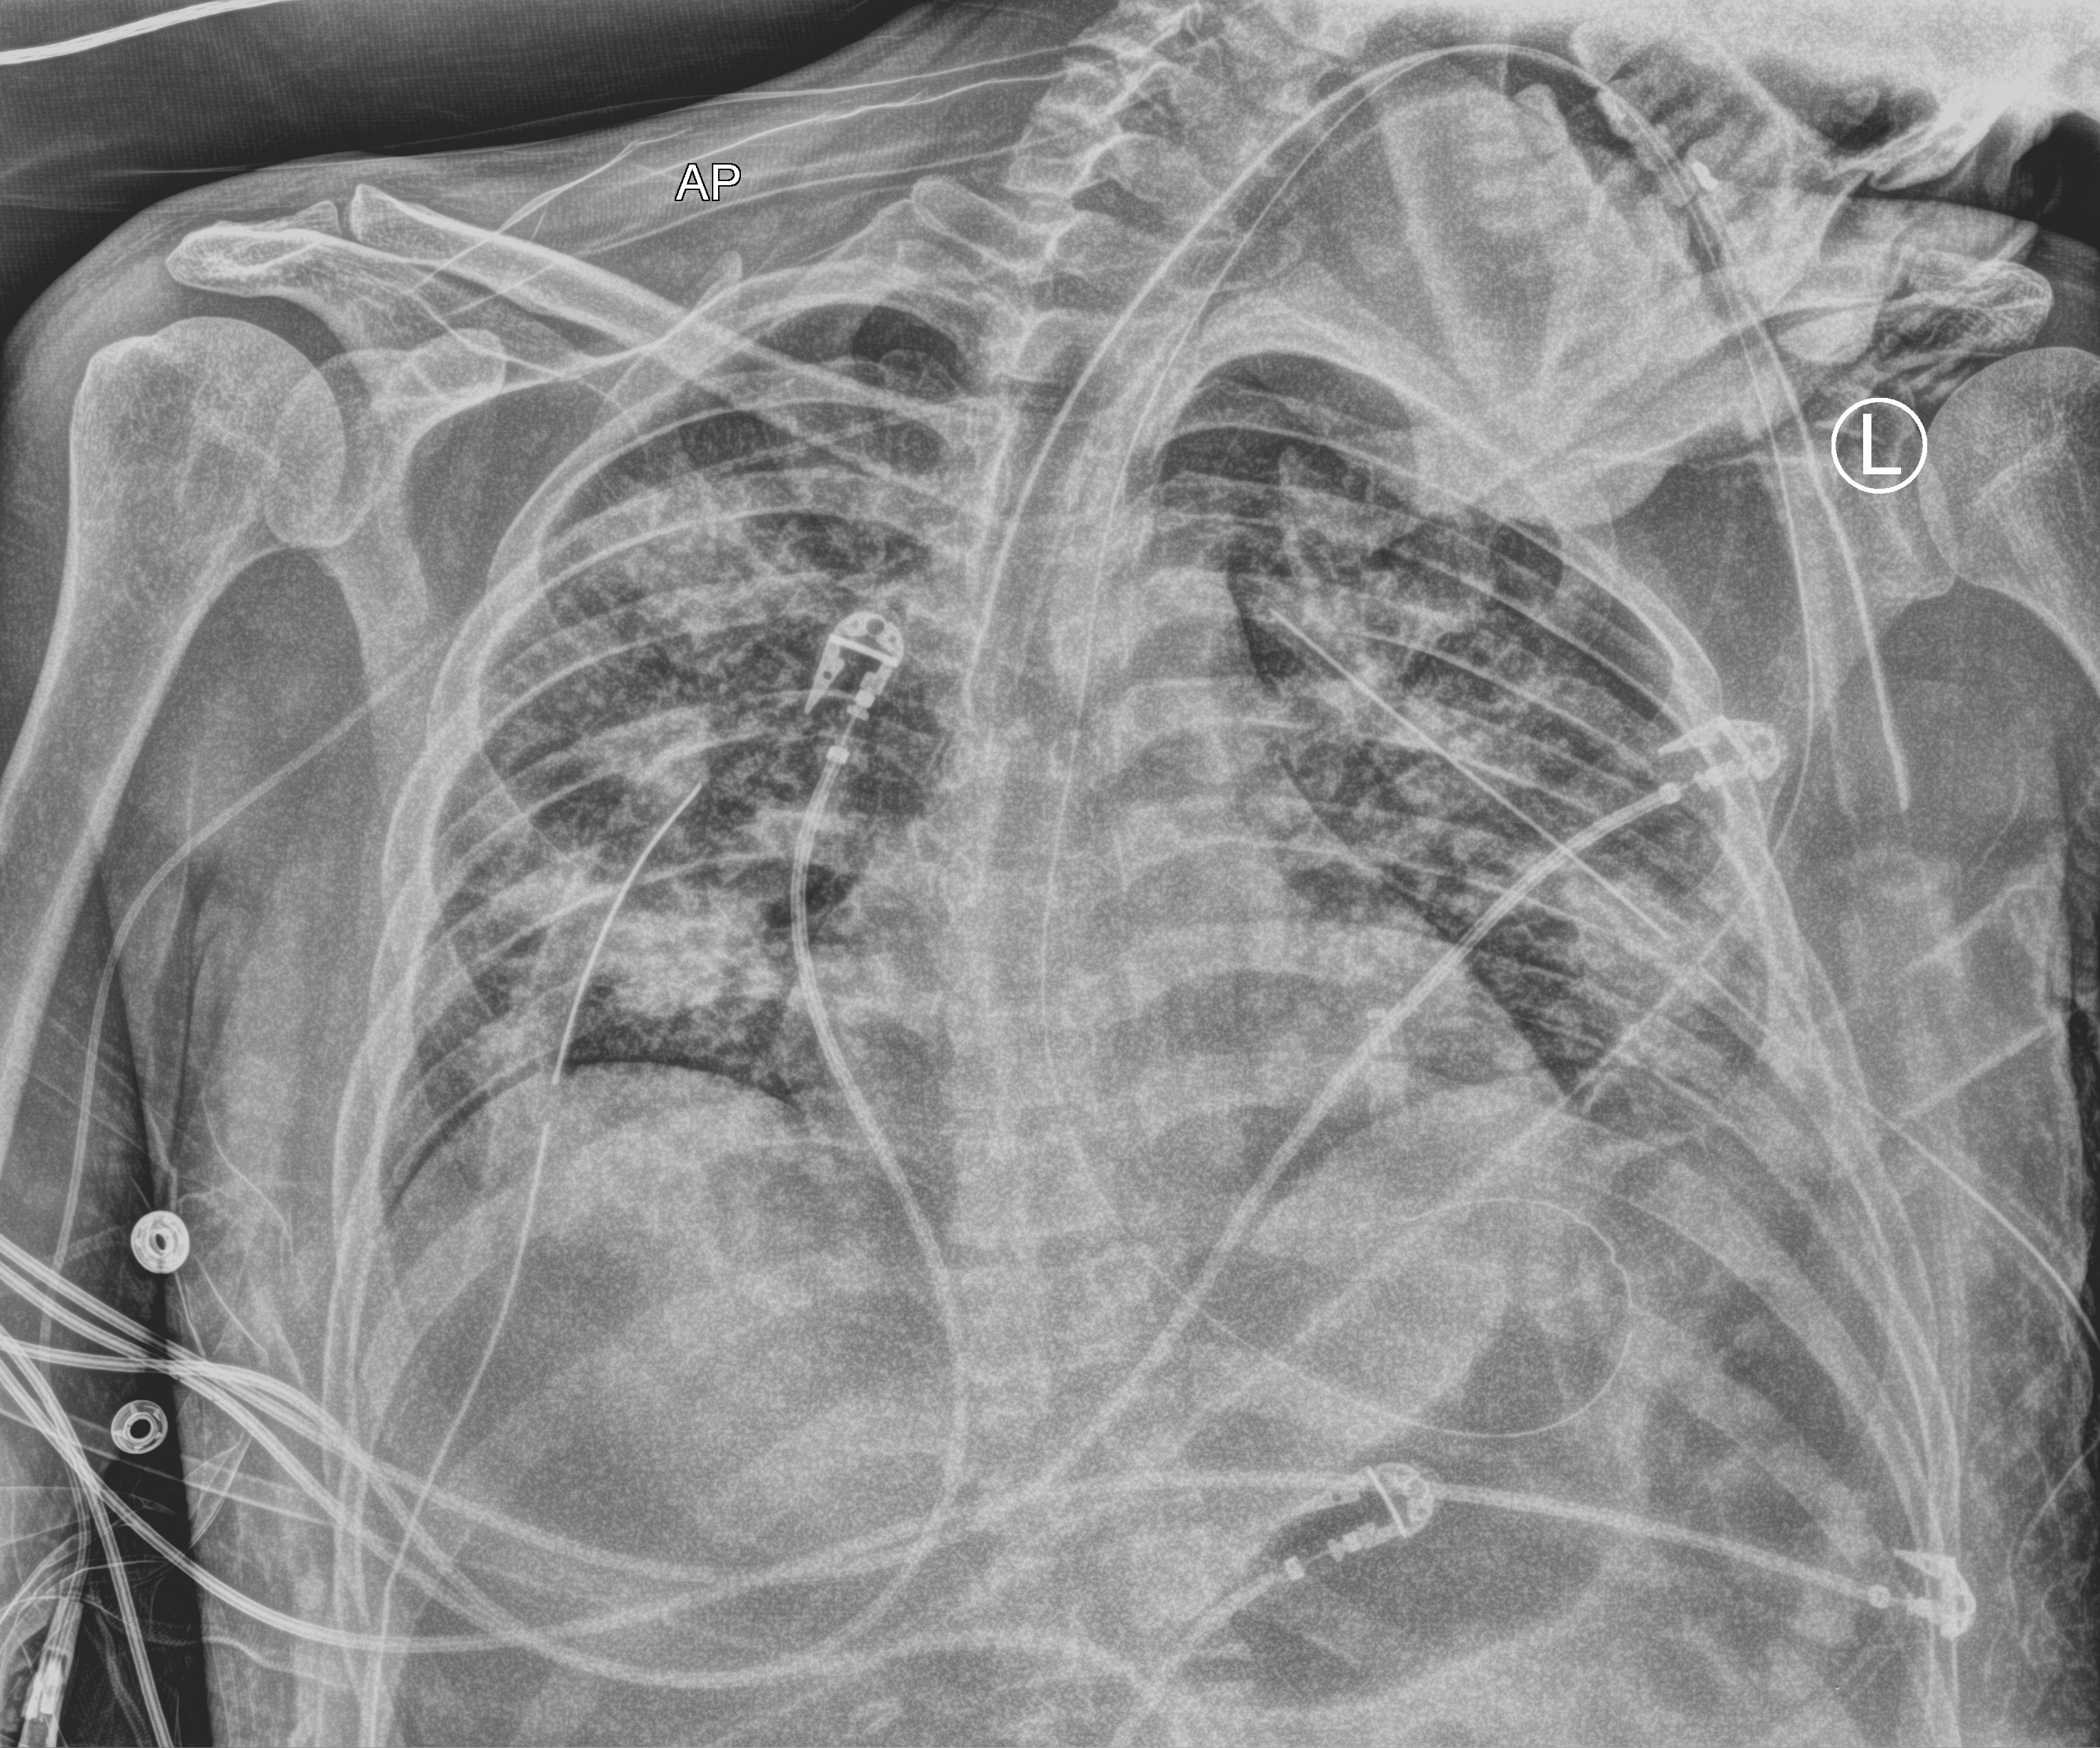
Chest X-ray (portable), anteroposterior (AP) projection. Patient hospitalised with COVID-19; male, aged 18–59 years.
From the hospital-stay record, not from the radiograph (when in the stay this image was taken is not recorded):
- mechanically ventilated during this hospital stay: yes